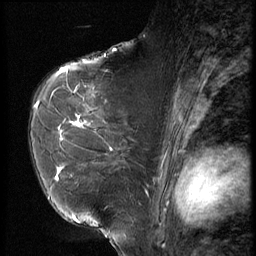
Breast MRI (dynamic contrast-enhanced), one sagittal slice; slice 40 of 56 in the series (ordered by position); 3 images stored at this slice position (order not interpretable as contrast timing); 1.5 T; TE 4.2 ms, TR 9 ms; 256 × 256 image matrix, field of view 180 × 180 mm. Female patient, age 61 years. From the clinical record (not read from this slice): setting: breast cancer imaged before/during neoadjuvant chemotherapy; receptor status: HR-positive, HER2-negative.
Annotated regions visible in this slice (semi-automatic segmentation, software-assisted and operator-edited):
- analysis volume of interest (the breast-tissue region the enhancement analysis was run in; not a lesion): box from (x=47, y=89) to (x=153, y=191) px
- tumour enhancement mask (voxels above the 140 % enhancement threshold inside the analysis volume of interest): (x=55, y=121)–(x=113, y=180)